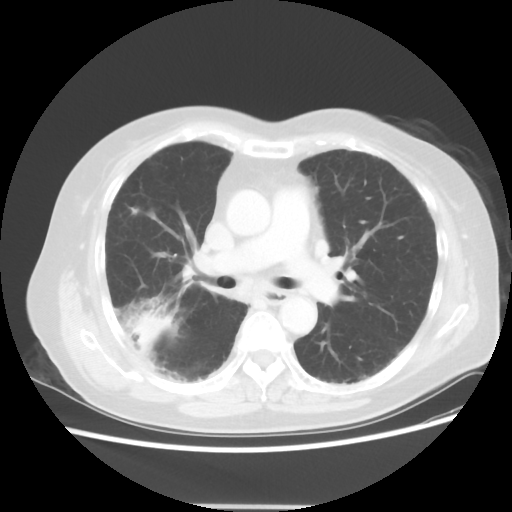
Chest CT, one axial slice; slice 28 of 50 in the series (ordered by position); reconstruction kernel STANDARD; lung window (W 1500 / L -600 HU); 5 mm slice thickness; 512 × 512 image matrix, field of view 360 × 360 mm. Patient: female, 72 years. From the clinical record (not read from this slice): clinical TNM (as recorded): T2 N1 M0; histopathological grade: G1.
Outlined on this slice (bounding box drawn by a radiologist):
- lung tumour (recorded histology: adenocarcinoma): bounding box (x1, y1, x2, y2) in pixels: (130, 311, 172, 351)